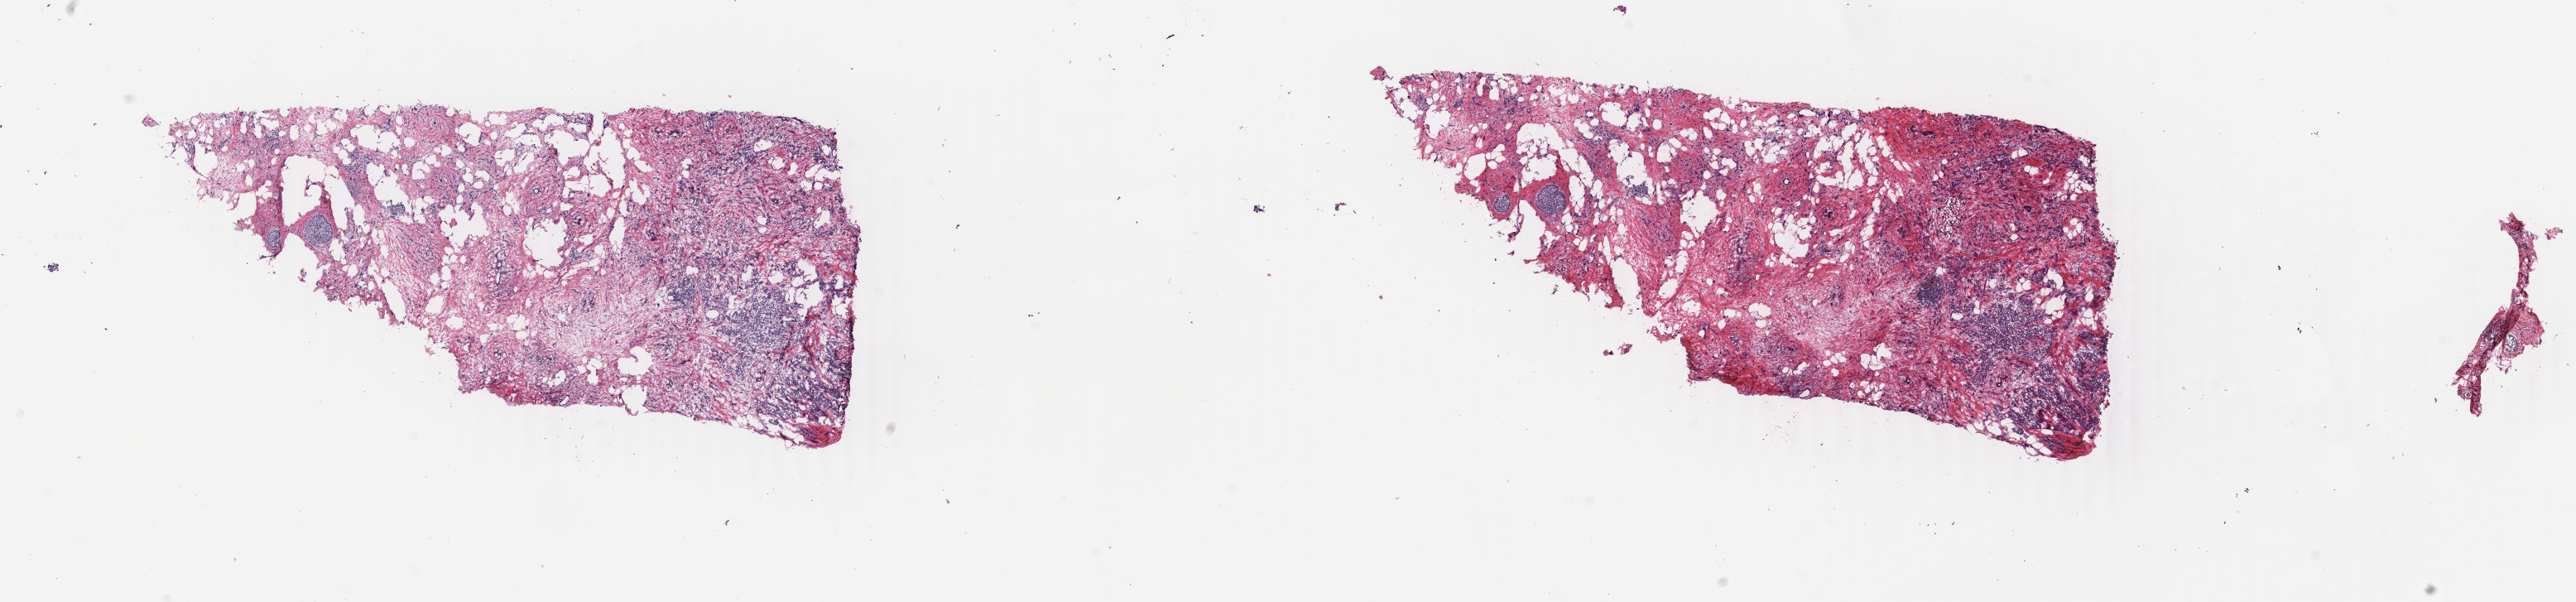
Whole-slide histology image, H&E-stained — low-resolution overview of the scanned area, about 24.7 x 5.8 mm. Frozen section. Sample: primary tumour, breast. Patient: female, age at initial diagnosis 62 years. Composition of this section per pathologist review: tumour cells 69%, tumour nuclei 70%, normal cells 20%, stromal cells 10%, necrosis 1%. Inflammatory infiltration, as recorded: lymphocyte infiltration 15%, monocyte infiltration 0%, neutrophil infiltration 0%.
• TNM: T1c N0 (i+) M0
• histologic diagnosis: Infiltrating duct and lobular carcinoma
• lymph nodes positive (case pathology): 0 of 3 examined
• AJCC pathologic stage: I (6th edition)